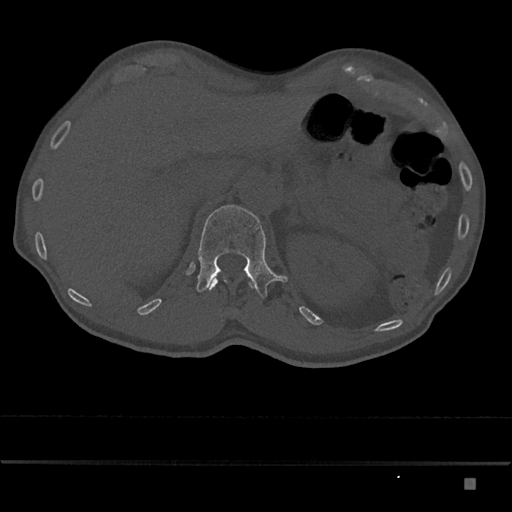
CT including the spine, one axial slice. Position 564 of 797 along the scan axis. Reconstruction kernel Br40s/3. Bone window (W 1800 / L 400 HU). 0.5 mm slice thickness. 512 × 512 image matrix, field of view 390 × 390 mm. Male patient, age 72 years. From the clinical record (not read from this slice): primary cancer: prostate.
Annotated regions visible in this slice (semi-automatically segmented with operator editing):
- L1 vertebra: bounding box <196,205,288,299> (left, top, right, bottom; pixels)
- T12 vertebra: <207,276,254,290>